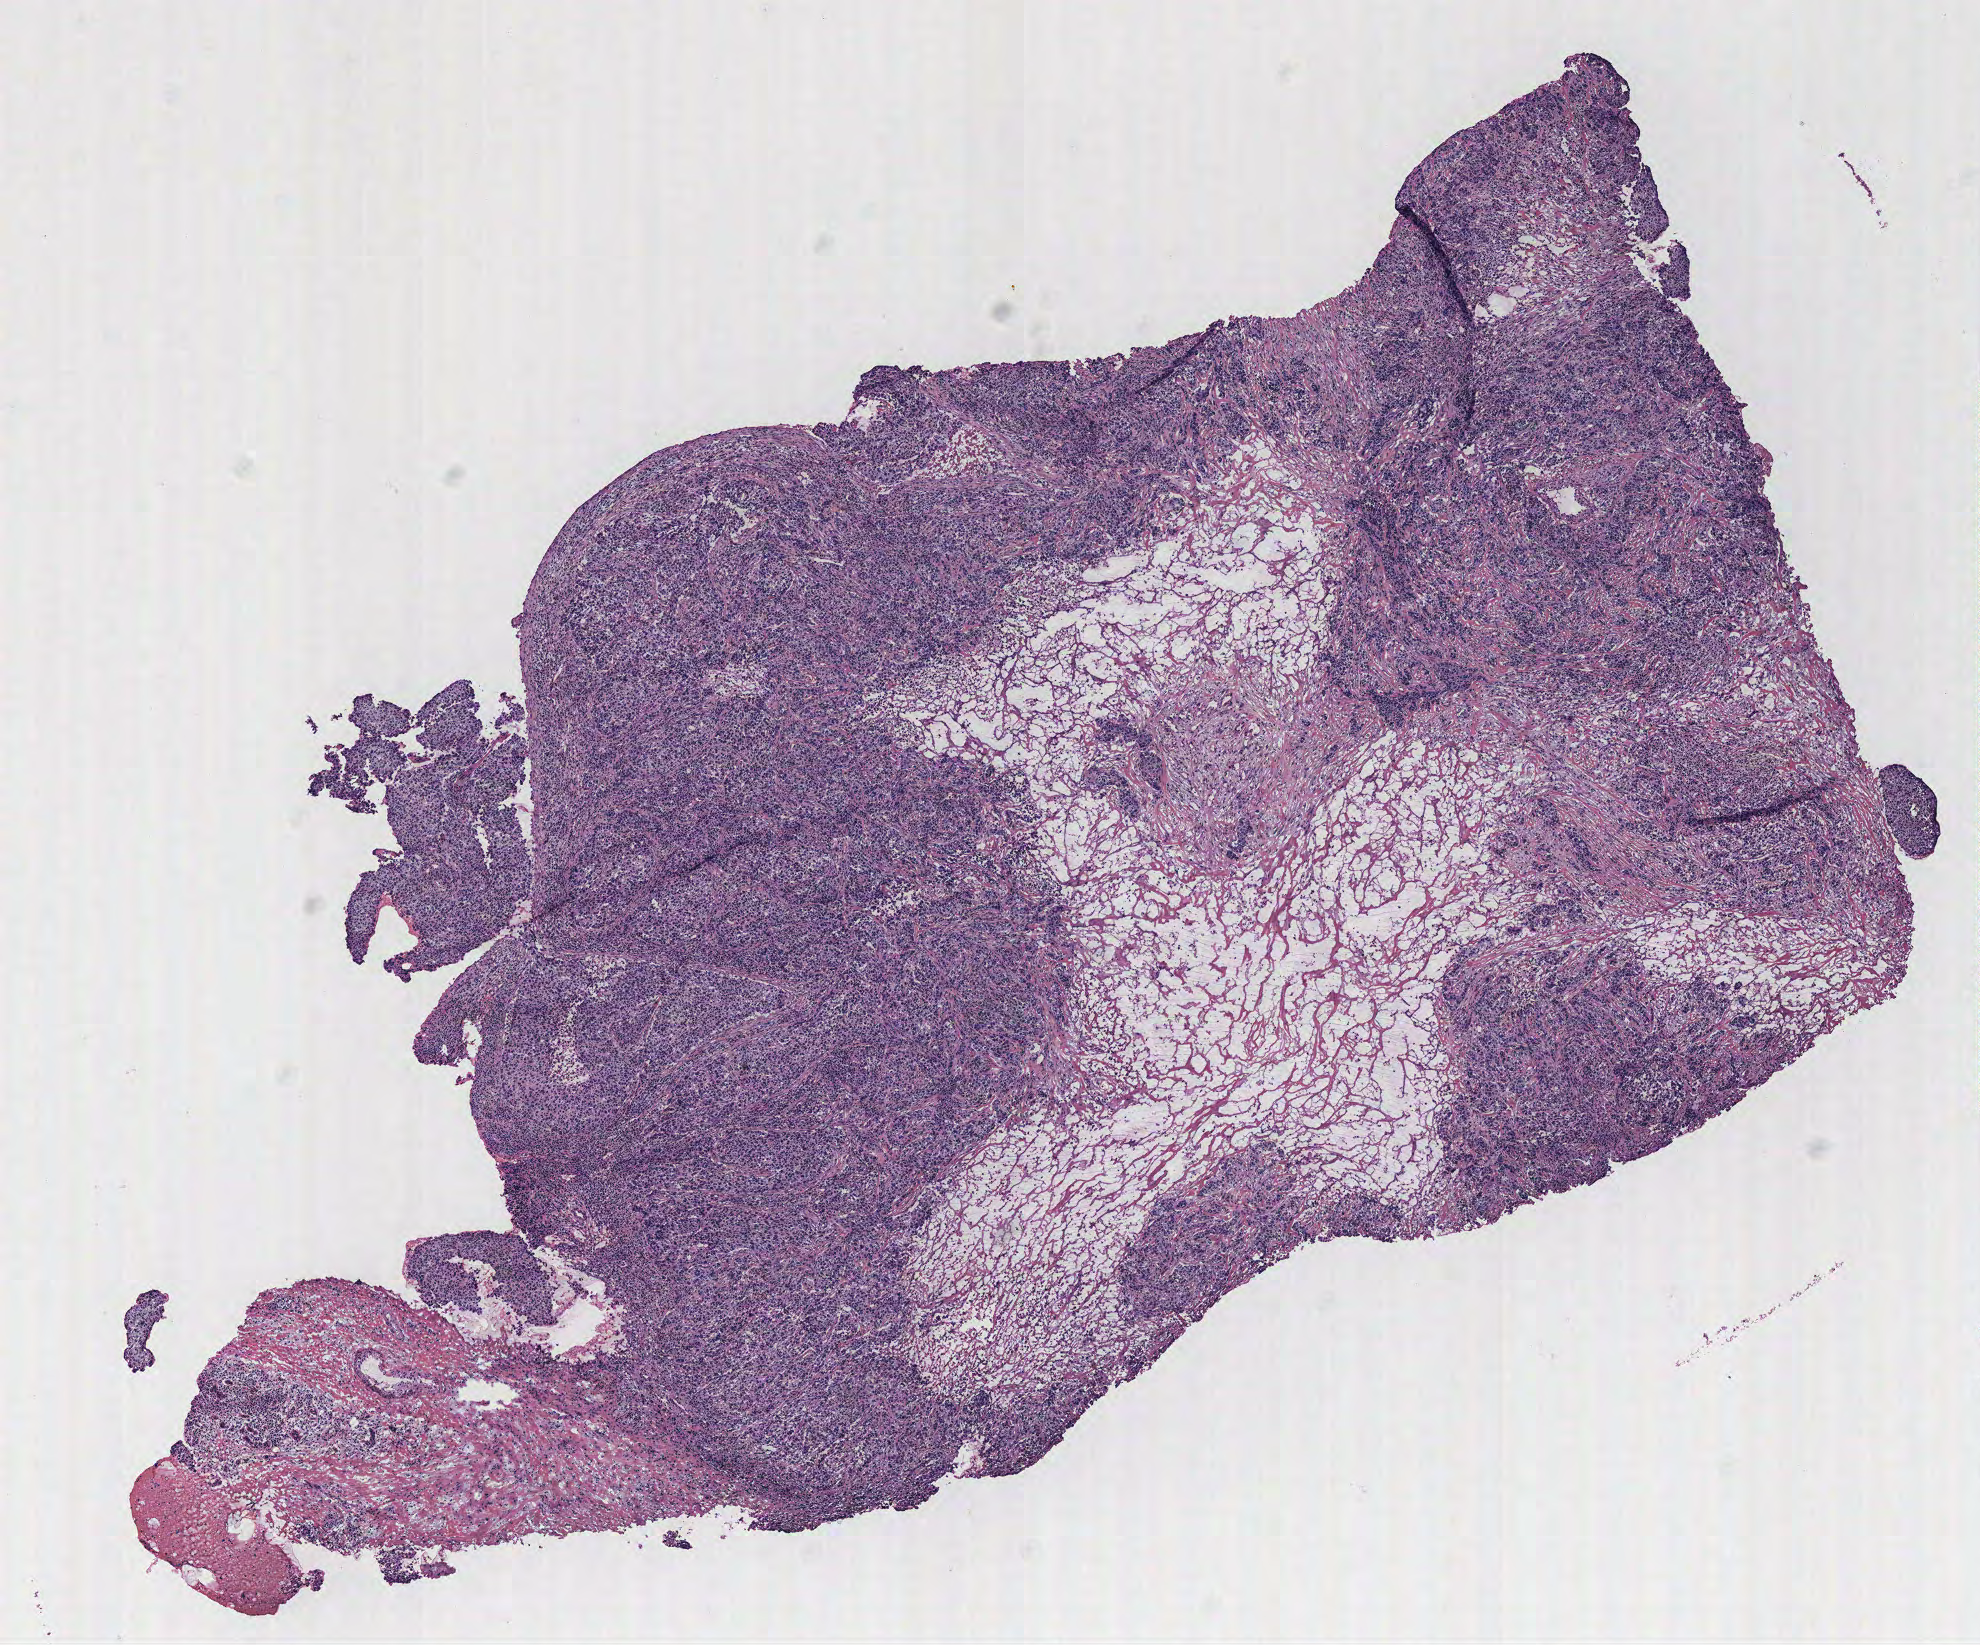
Whole-slide histology image, H&E — shown as a low-resolution overview of the whole scanned area (about 7.9 x 6.6 mm, acquisition: 40x scan). Breast, tissue type not recorded. 53-year-old female patient.
Patient diagnosis: Infiltrating duct carcinoma, NOS.